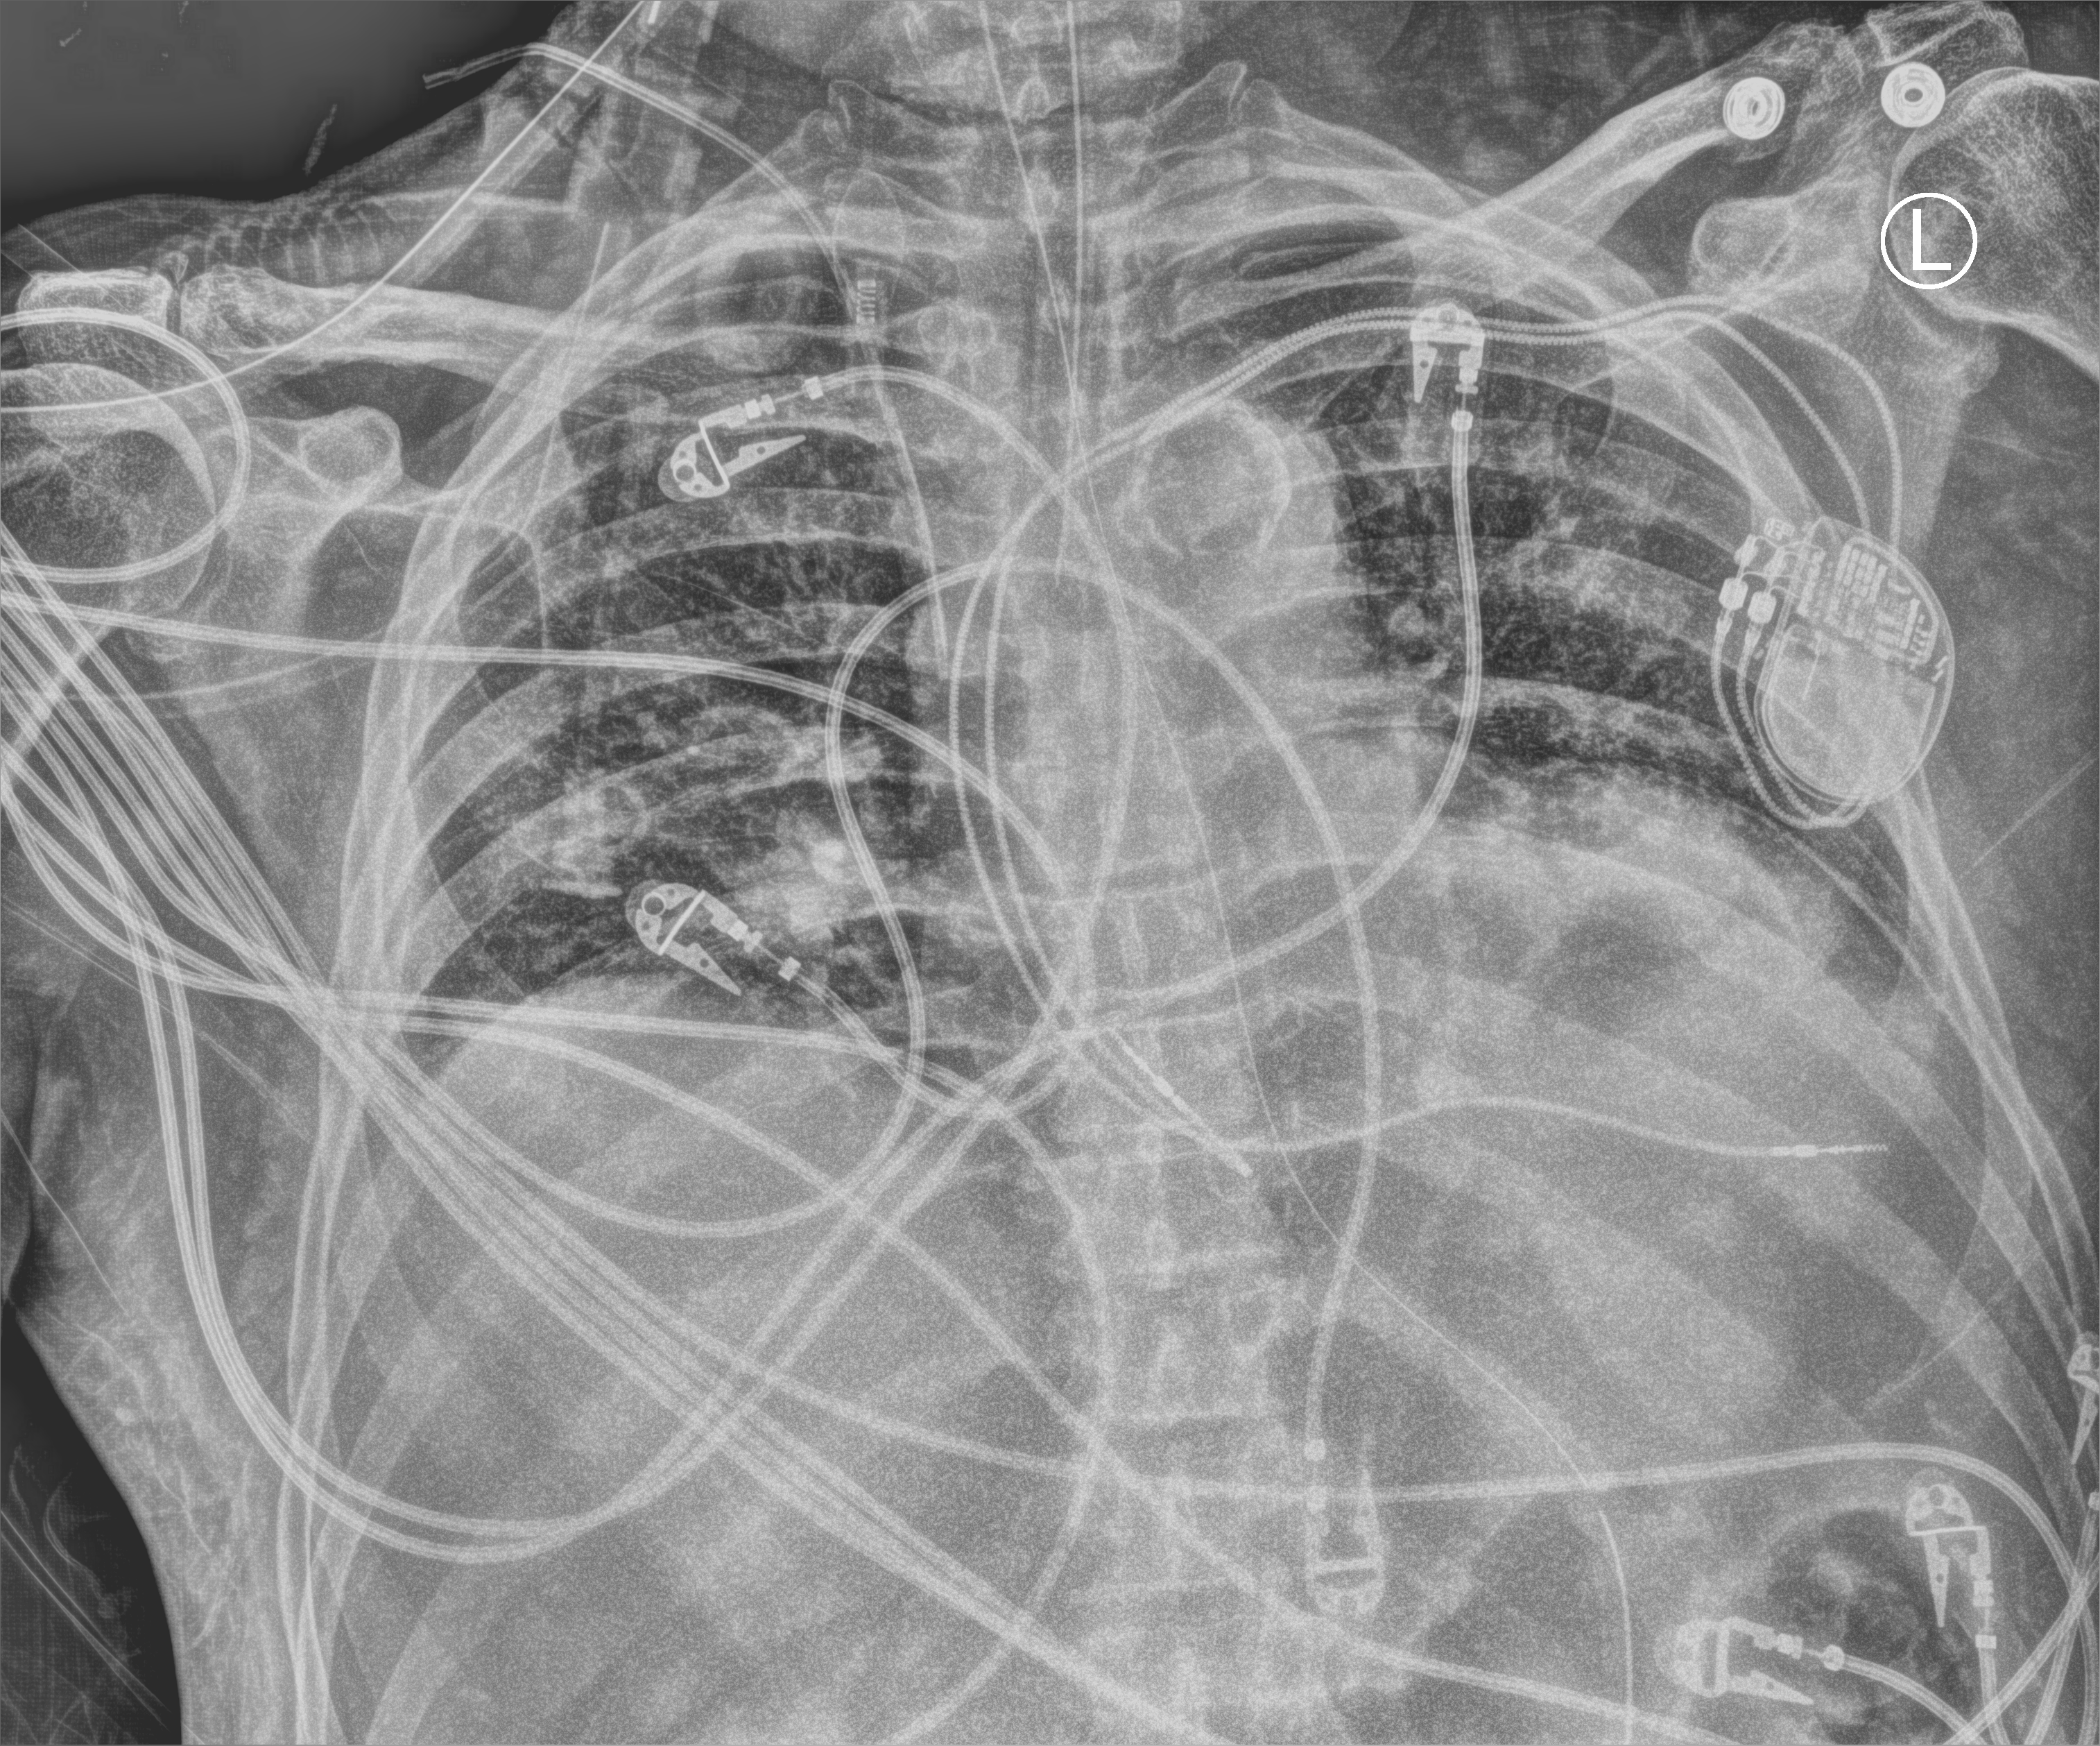
Portable chest radiograph, anteroposterior (AP) projection. Male patient hospitalised with COVID-19, age 60–74 years.
Hospital-stay facts (about this admission, not read from this image; timing relative to this image not recorded): admitted to intensive care during this hospital stay: yes; mechanically ventilated during this hospital stay: yes.